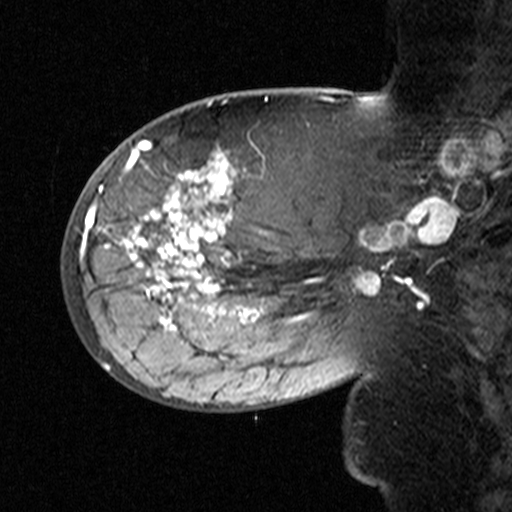
Breast MRI (dynamic contrast-enhanced), one sagittal slice; position 17 of 44 along the scan axis; dynamic contrast-enhanced study with each time point stored as its own series, time point 2 of 3 at this slice position (early post-contrast, ordered by acquisition time); 1.5 T; TE 4.5 ms, TR 11 ms; 512 × 512 image matrix. Female patient, age 53 years. From the clinical record (not read from this slice): setting: breast cancer imaged before/during neoadjuvant chemotherapy; receptor status: HR-positive, HER2-negative.
Structures marked on this image (semi-automatic segmentation, software-assisted and operator-edited):
- analysis volume of interest (the breast-tissue region the enhancement analysis was run in; not a lesion): bounding box (x1, y1, x2, y2) in pixels: (76, 140, 311, 353)
- tumour enhancement mask (voxels above the 90 % enhancement threshold inside the analysis volume of interest): (79, 145, 310, 334)